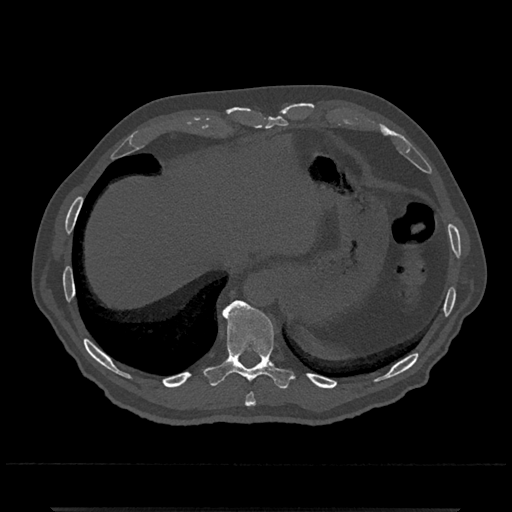
CT including the spine, one axial slice; position 557 of 797 along the scan axis; bone window (W 1800 / L 400 HU); 512 × 512 image matrix, field of view 393 × 393 mm. Male patient, age 67 years. Case-level facts recorded for this patient, not image findings: primary cancer: prostate.
Annotated regions visible in this slice (semi-automatic segmentation, software-assisted and operator-edited):
- T10 vertebra: bounding box (x1, y1, x2, y2) in pixels: (204, 300, 293, 389)
- T9 vertebra: (245, 393, 256, 407)